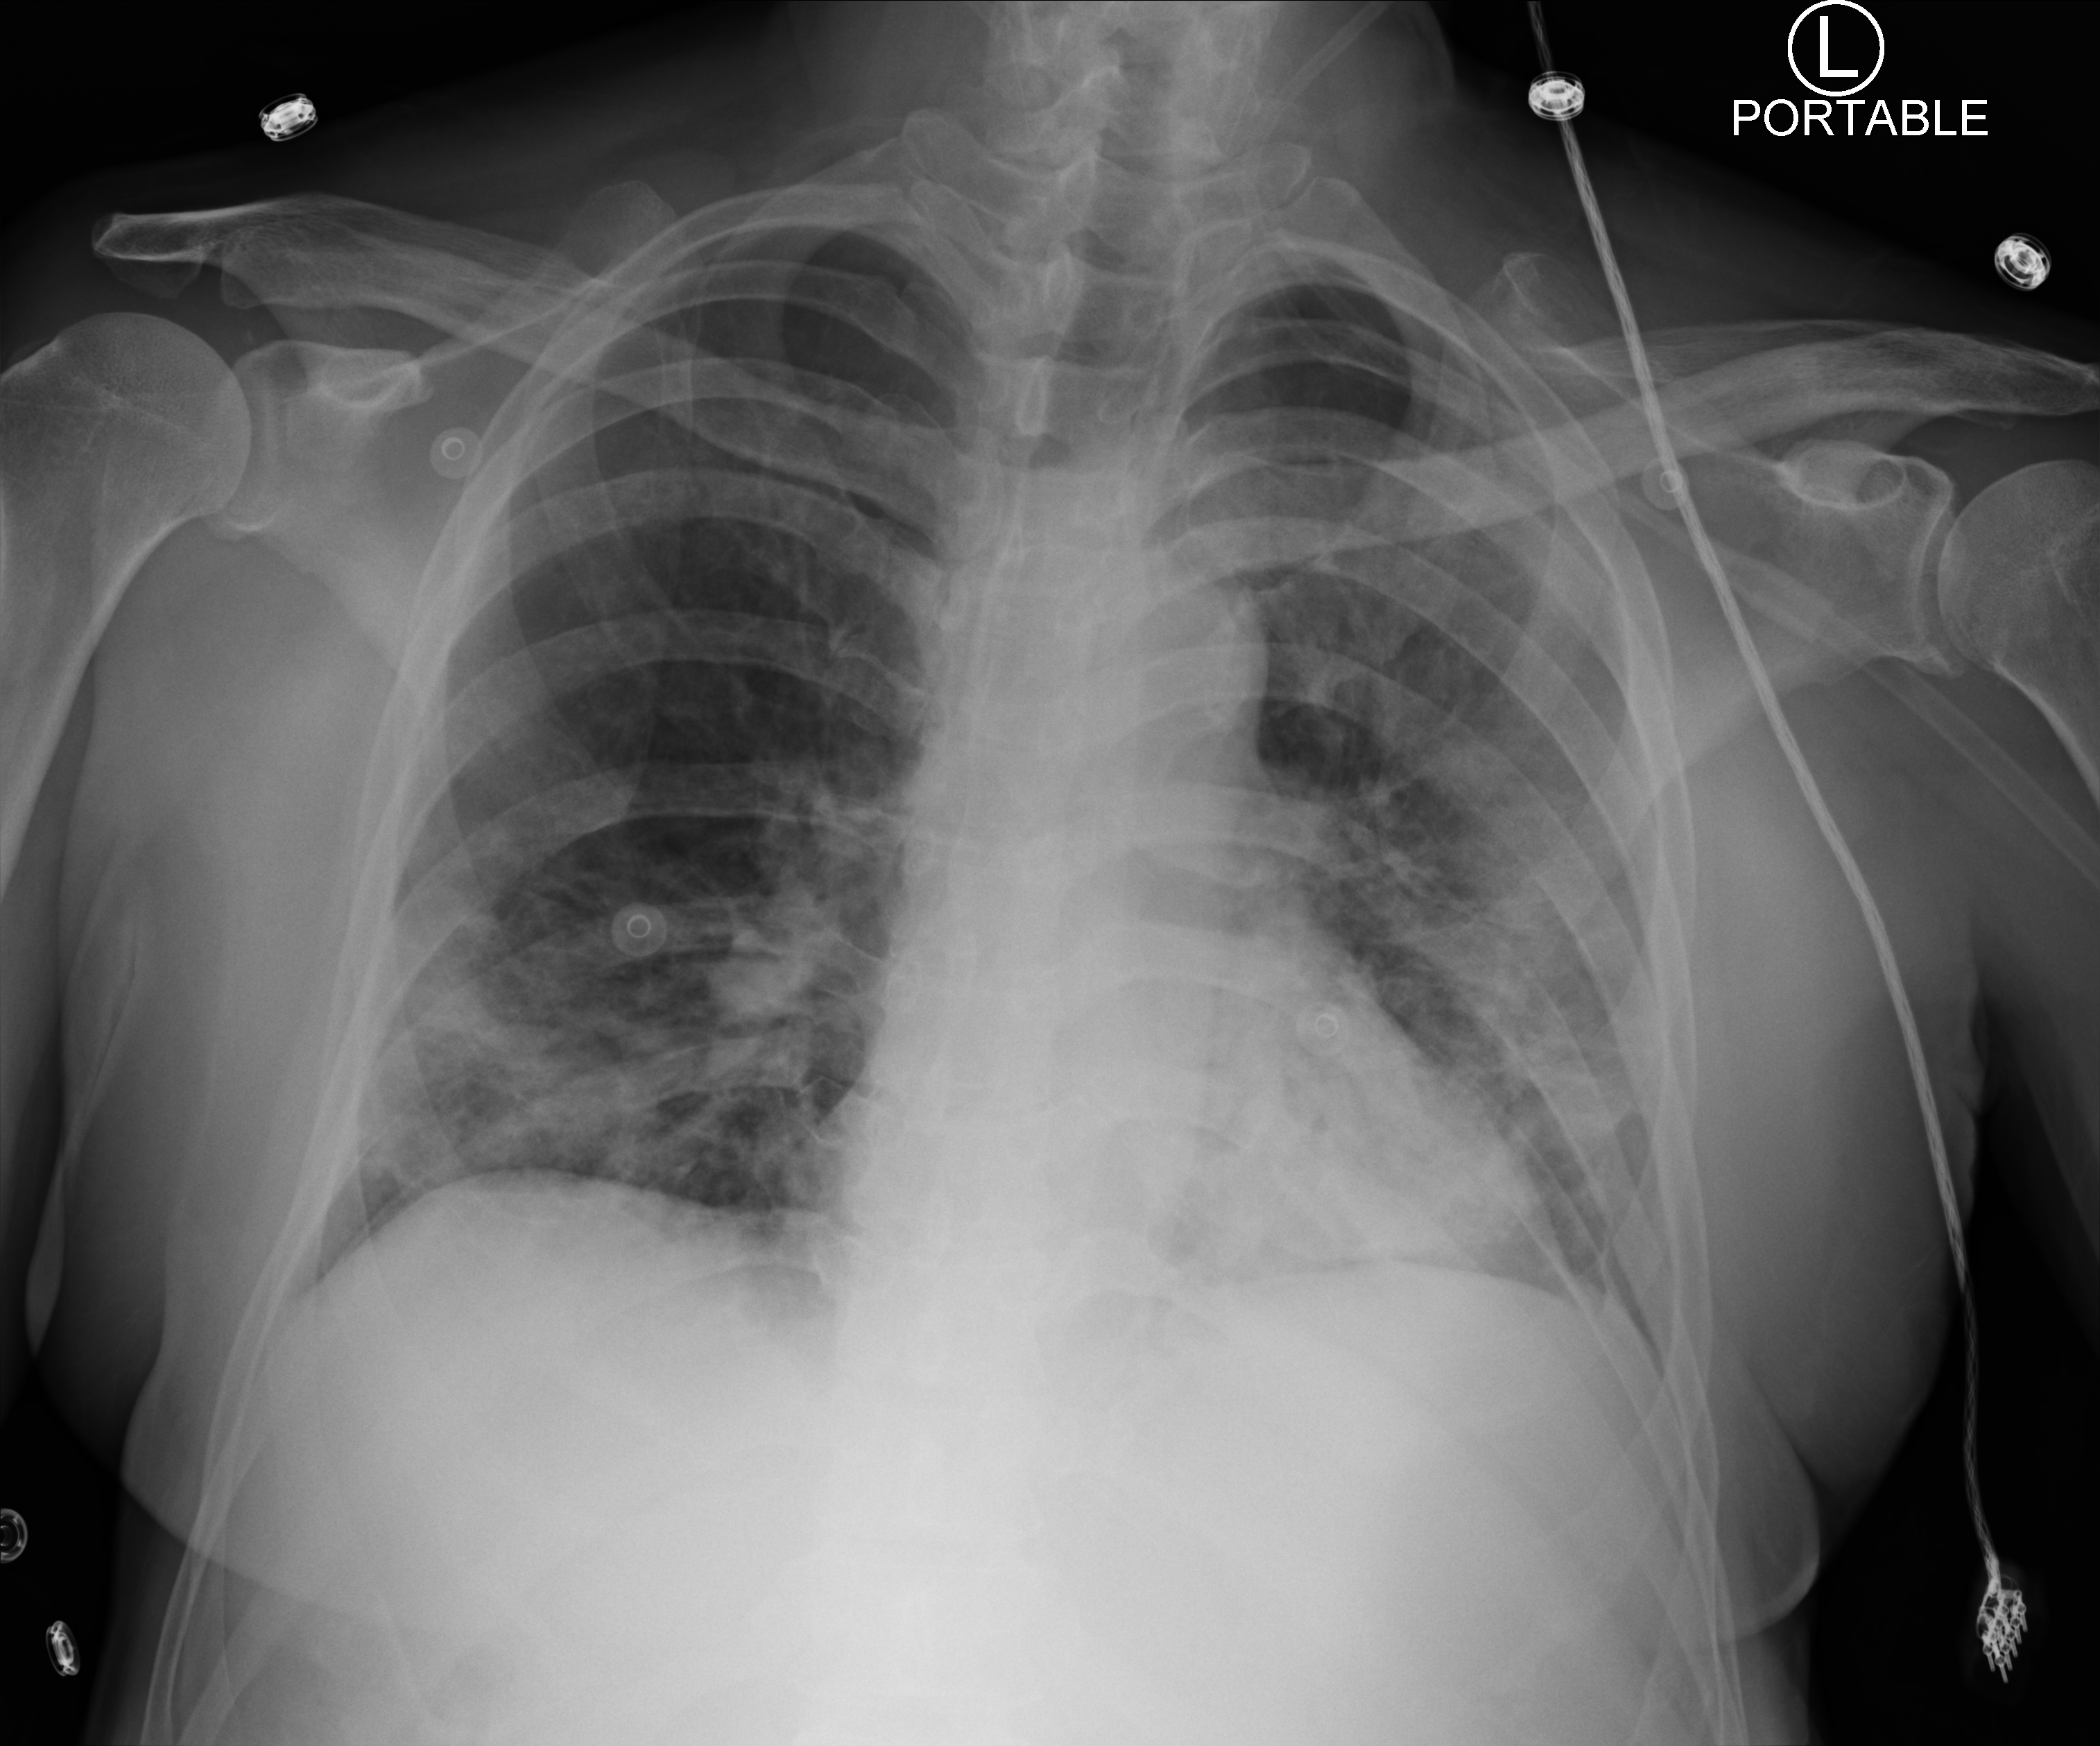
Bedside chest radiograph (computed radiography); anteroposterior (AP) projection. Male patient hospitalised with COVID-19, age 60–74 years.
Hospital-stay facts (about this admission, not read from this image; timing relative to this image not recorded): length of hospital stay: 10 days; hypertension (admission record): yes.